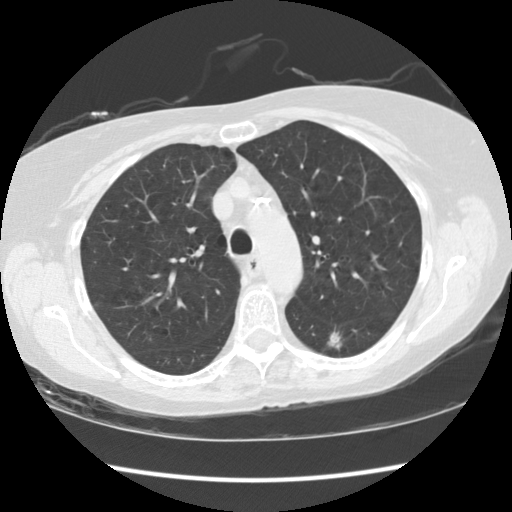
Low-dose screening chest CT, one axial slice. Slice 86 of 119 in the series (ordered by position). Reconstruction kernel STANDARD. Lung window (W 1500 / L -600 HU). 512 × 512 image matrix, field of view 334 × 334 mm.
Structures marked on this image (expert manual segmentation):
- lesion 1 (tumor, lower lobe of left lung): bounding box [x1, y1, x2, y2] px = [328, 331, 342, 349]